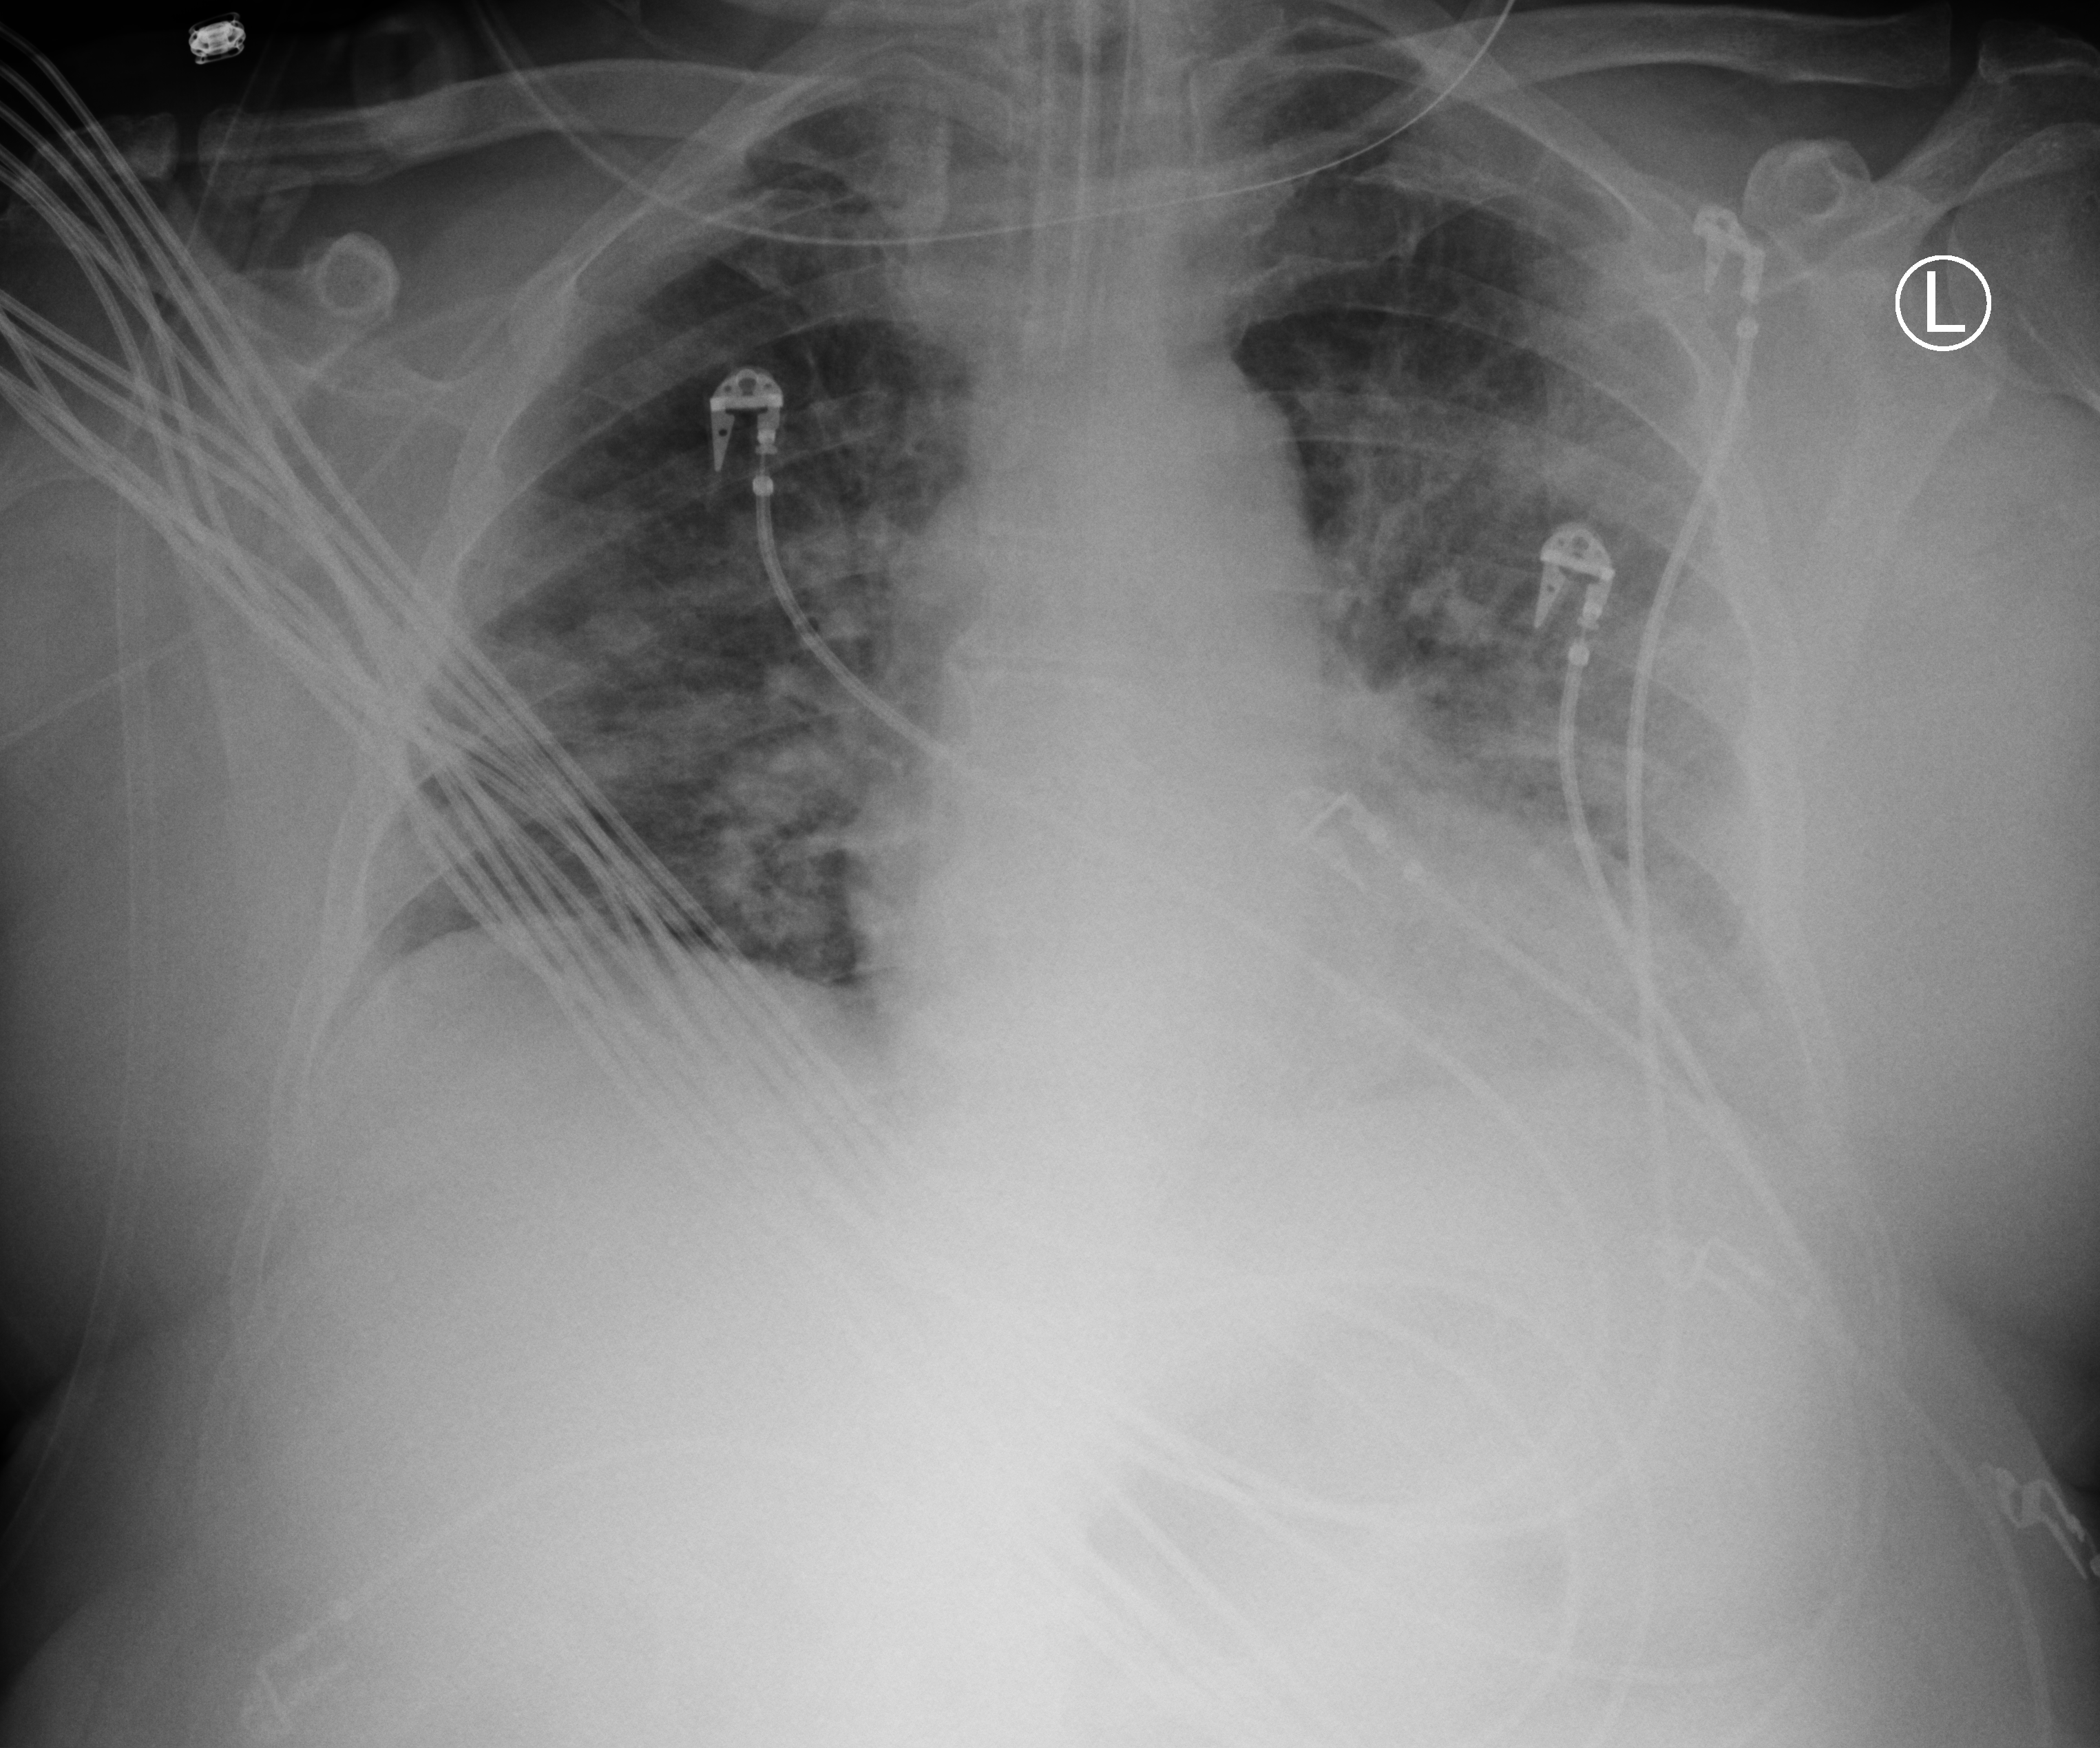
Chest X-ray (portable); anteroposterior (AP) projection. Male patient hospitalised with COVID-19, age 60–74 years.
Admission-level facts for this patient (not findings on this image; timing relative to this image not recorded): admitted to intensive care during this hospital stay: yes; other chronic lung disease (admission record): no; mechanically ventilated during this hospital stay: yes.